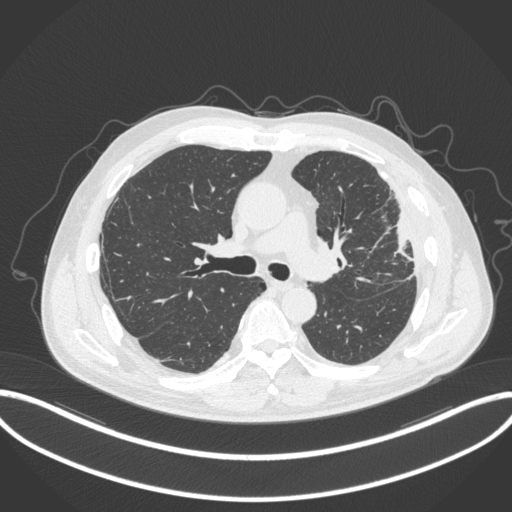
Chest CT, one axial slice. Position 212 of 382 along the scan axis. 120 kVp. Lung window (W 1500 / L -600 HU). 1 mm slice thickness. 512 × 512 image matrix. Patient: male, 64 years. From the clinical record (not read from this slice): clinical TNM (as recorded): T4 N1 M0; histopathological grade: G3.
Annotated regions visible in this slice (bounding box drawn by a radiologist):
- lung tumour (recorded histology: adenocarcinoma): bounding box (x1, y1, x2, y2) in pixels: (387, 210, 419, 263)